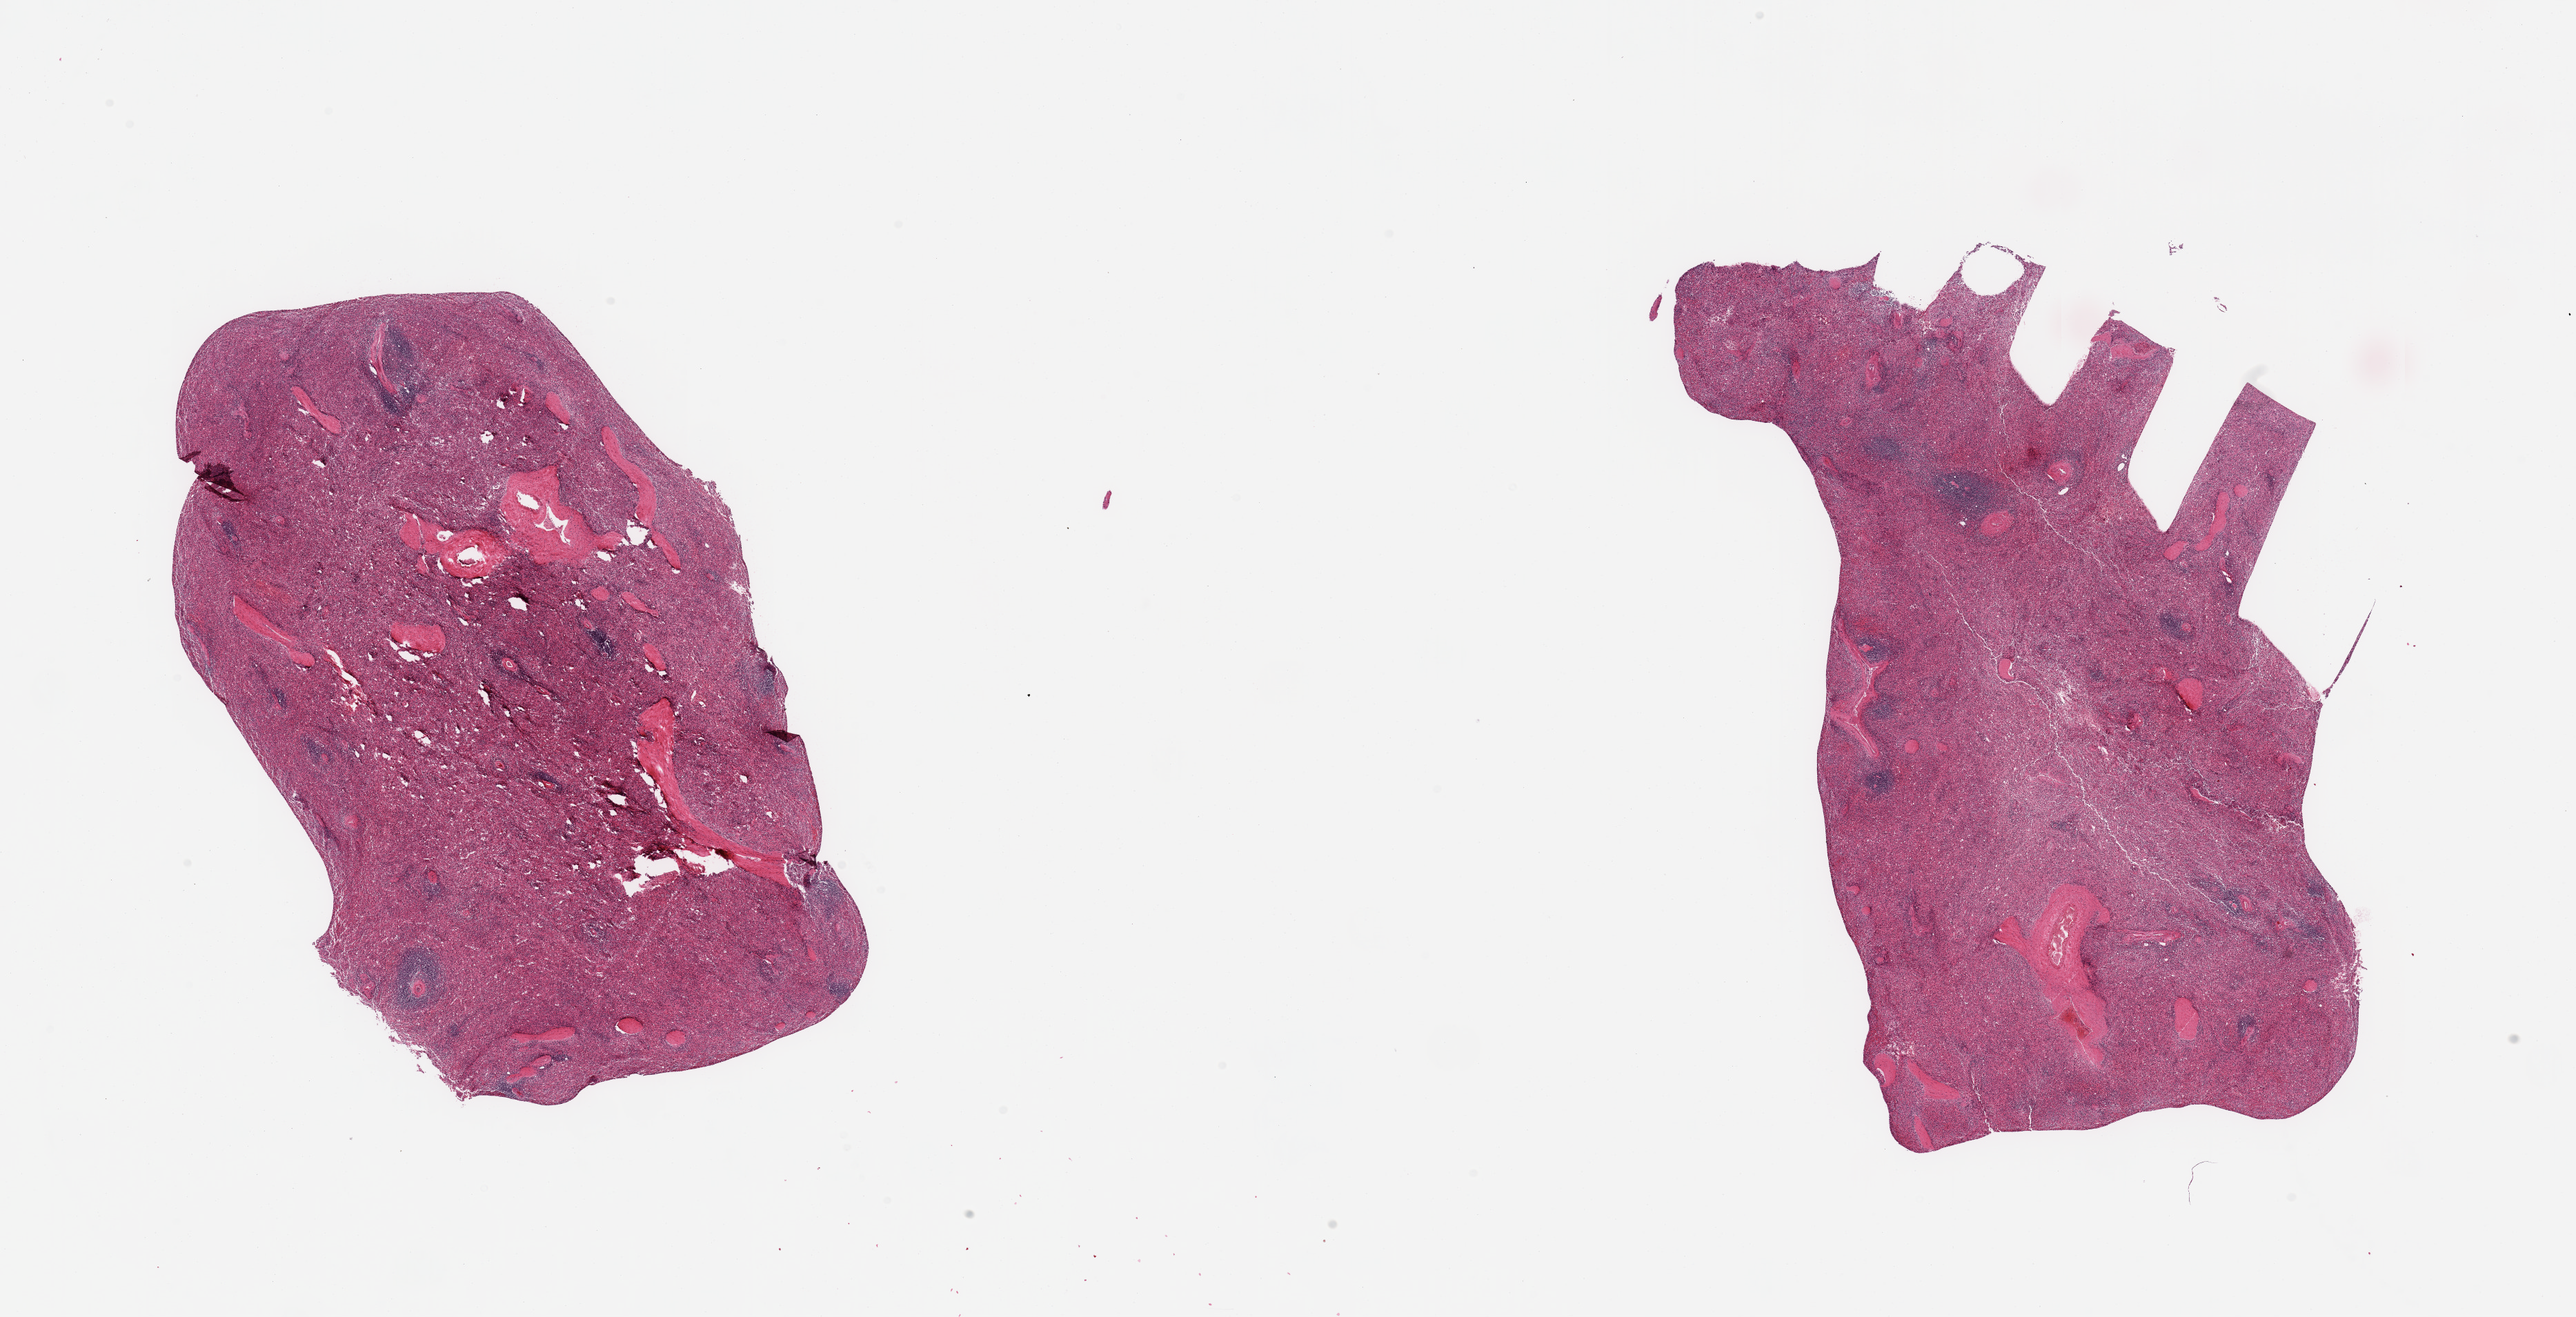
Digitized haematoxylin and eosin-stained section, low-resolution overview of the scanned area, about 29.5 x 15.1 mm, PAXgene-fixed paraffin-embedded (PFPE) section, target tissue: spleen, donor tissue sample. Male donor.
Pathologist's review note for this sample: 2 pieces, no abnormalities.